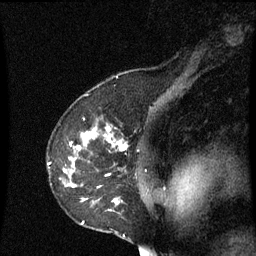
Breast MRI (dynamic contrast-enhanced), one sagittal slice. Slice 47 of 60 in the series (ordered by position). Dynamic contrast-enhanced series, image 2 of 3 at this slice position (ordered by acquisition). 1.5 T. TE 4.2 ms, TR 8.9 ms. 256 × 256 image matrix, field of view 200 × 200 mm. Patient: female, 53 years. From the clinical record (not read from this slice): setting: breast cancer imaged before/during neoadjuvant chemotherapy; receptor status: HR-positive, HER2-negative.
Outlined on this slice (semi-automatically segmented with operator editing):
- analysis volume of interest (the breast-tissue region the enhancement analysis was run in; not a lesion): bounding box [x1, y1, x2, y2] px = [48, 128, 157, 231]
- tumour enhancement mask (voxels above the 70 % enhancement threshold inside the analysis volume of interest): [76, 128, 127, 205]